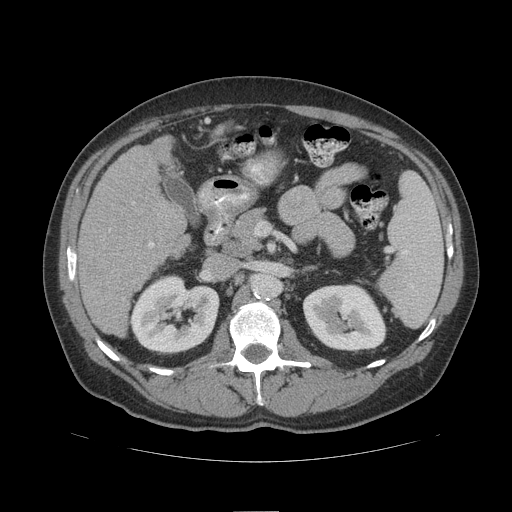
Contrast-enhanced abdominal CT (liver protocol), one axial slice. Slice 53 of 109 in the series (ordered by position). 140 kVp. Soft-tissue window (W 400 / L 40 HU). 512 × 512 image matrix, field of view 420 × 420 mm. Case-level facts recorded for this patient, not image findings: diagnosis: hepatocellular carcinoma (patient treated with transarterial chemoembolisation; whether this scan precedes or follows treatment is not stated here); TNM stage (as recorded): Stage-IIIB; Child-Pugh class: A.
Outlined on this slice (semi-automatically segmented with operator editing):
- liver parenchyma outside the tumour (the mass and vessels are separate outlines, so this box may not span the whole liver): box from (x=78, y=136) to (x=186, y=336) px
- liver vessels: (x=149, y=242)–(x=154, y=247)